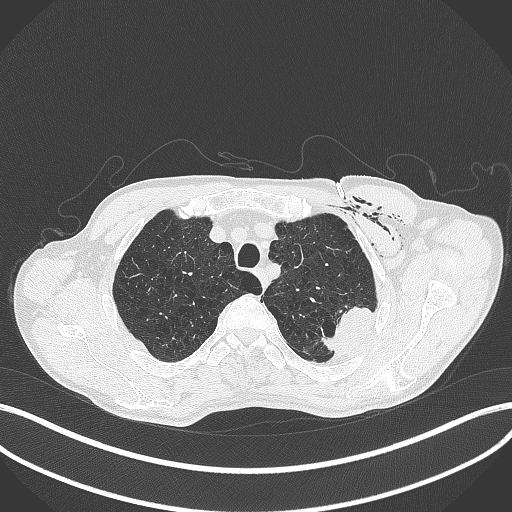
Chest CT, one axial slice. Slice 347 of 457 in the series (ordered by position). Reconstruction kernel B70f. 120 kVp. Lung window (W 1500 / L -600 HU). 1 mm slice thickness. 512 × 512 image matrix. Patient: male, 58 years. From the clinical record (not read from this slice): clinical TNM (as recorded): T3 N0 M0.
Outlined on this slice (bounding box drawn by a radiologist):
- lung tumour (recorded histology: adenocarcinoma): bounding box (x1, y1, x2, y2) in pixels: (319, 297, 378, 358)